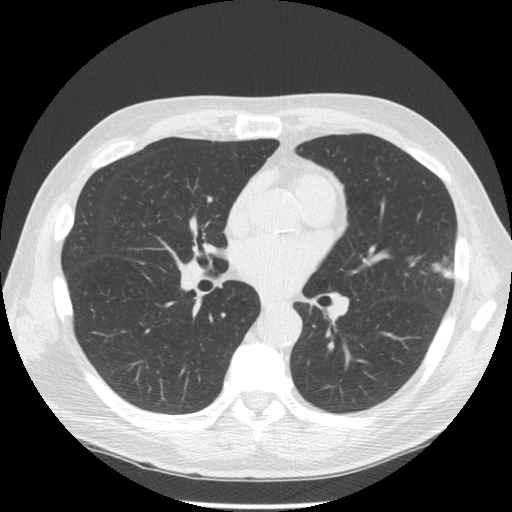
Low-dose screening chest CT, one axial slice. 120 kVp. Lung window (W 1500 / L -600 HU). 512 × 512 image matrix, field of view 350 × 350 mm.
Structures marked on this image (outlined manually by an expert reader):
- lesion 1 (tumor, upper lobe of left lung): box from (x=433, y=263) to (x=455, y=279) px